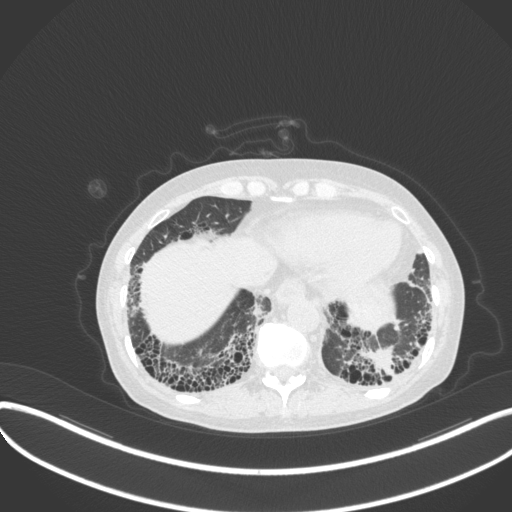
Chest CT, one axial slice. Position 64 of 373 along the scan axis. Reconstruction kernel B31f. 120 kVp. Lung window (W 1500 / L -600 HU). 1 mm slice thickness. 512 × 512 image matrix, field of view 400 × 400 mm. Patient: female, 56 years. Case-level facts recorded for this patient, not image findings: clinical TNM (as recorded): T1 N0 M0.
Outlined on this slice (rectangle marked by the reading radiologist):
- lung tumour (recorded histology: adenocarcinoma): bounding box [x1, y1, x2, y2] px = [361, 344, 401, 385]